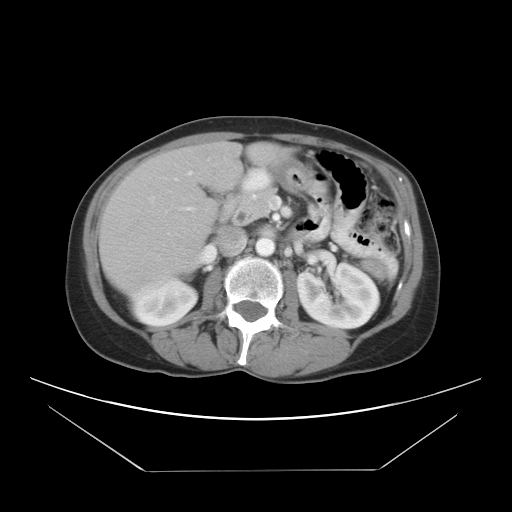
Contrast-enhanced abdominal CT, one axial slice. Slice 13 of 30 in the series (ordered by position). Reconstruction kernel STANDARD. Intravenous contrast given. Soft-tissue window (W 400 / L 40 HU). 7.5 mm slice thickness. 512 × 512 image matrix, field of view 412 × 412 mm. Female patient, age 54 years. From the clinical record (not read from this slice): diagnosis: colorectal cancer liver metastases, imaged before liver resection; multiple liver metastases: yes; largest metastasis: 2.5 cm.
Outlined on this slice (outlined manually by an expert reader):
- liver: box from (x=101, y=143) to (x=276, y=291) px
- planned liver remnant (the part of the liver to remain after resection): (x=116, y=143)–(x=243, y=280)
- portal vein (with intrahepatic branches): (x=173, y=170)–(x=195, y=182)